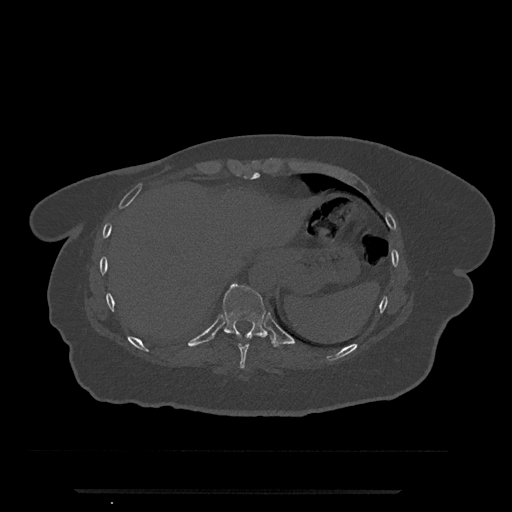
CT including the spine, one axial slice. Position 307 of 797 along the scan axis. 120 kVp. Bone window (W 1800 / L 400 HU). 0.5 mm slice thickness. 512 × 512 image matrix, field of view 440 × 440 mm. Patient: female, 51 years. From the clinical record (not read from this slice): primary cancer: neuro.
Annotated regions visible in this slice (semi-automatically segmented with operator editing):
- T10 vertebra: box from (x=223, y=283) to (x=277, y=347) px
- T9 vertebra: (x=238, y=343)–(x=250, y=369)